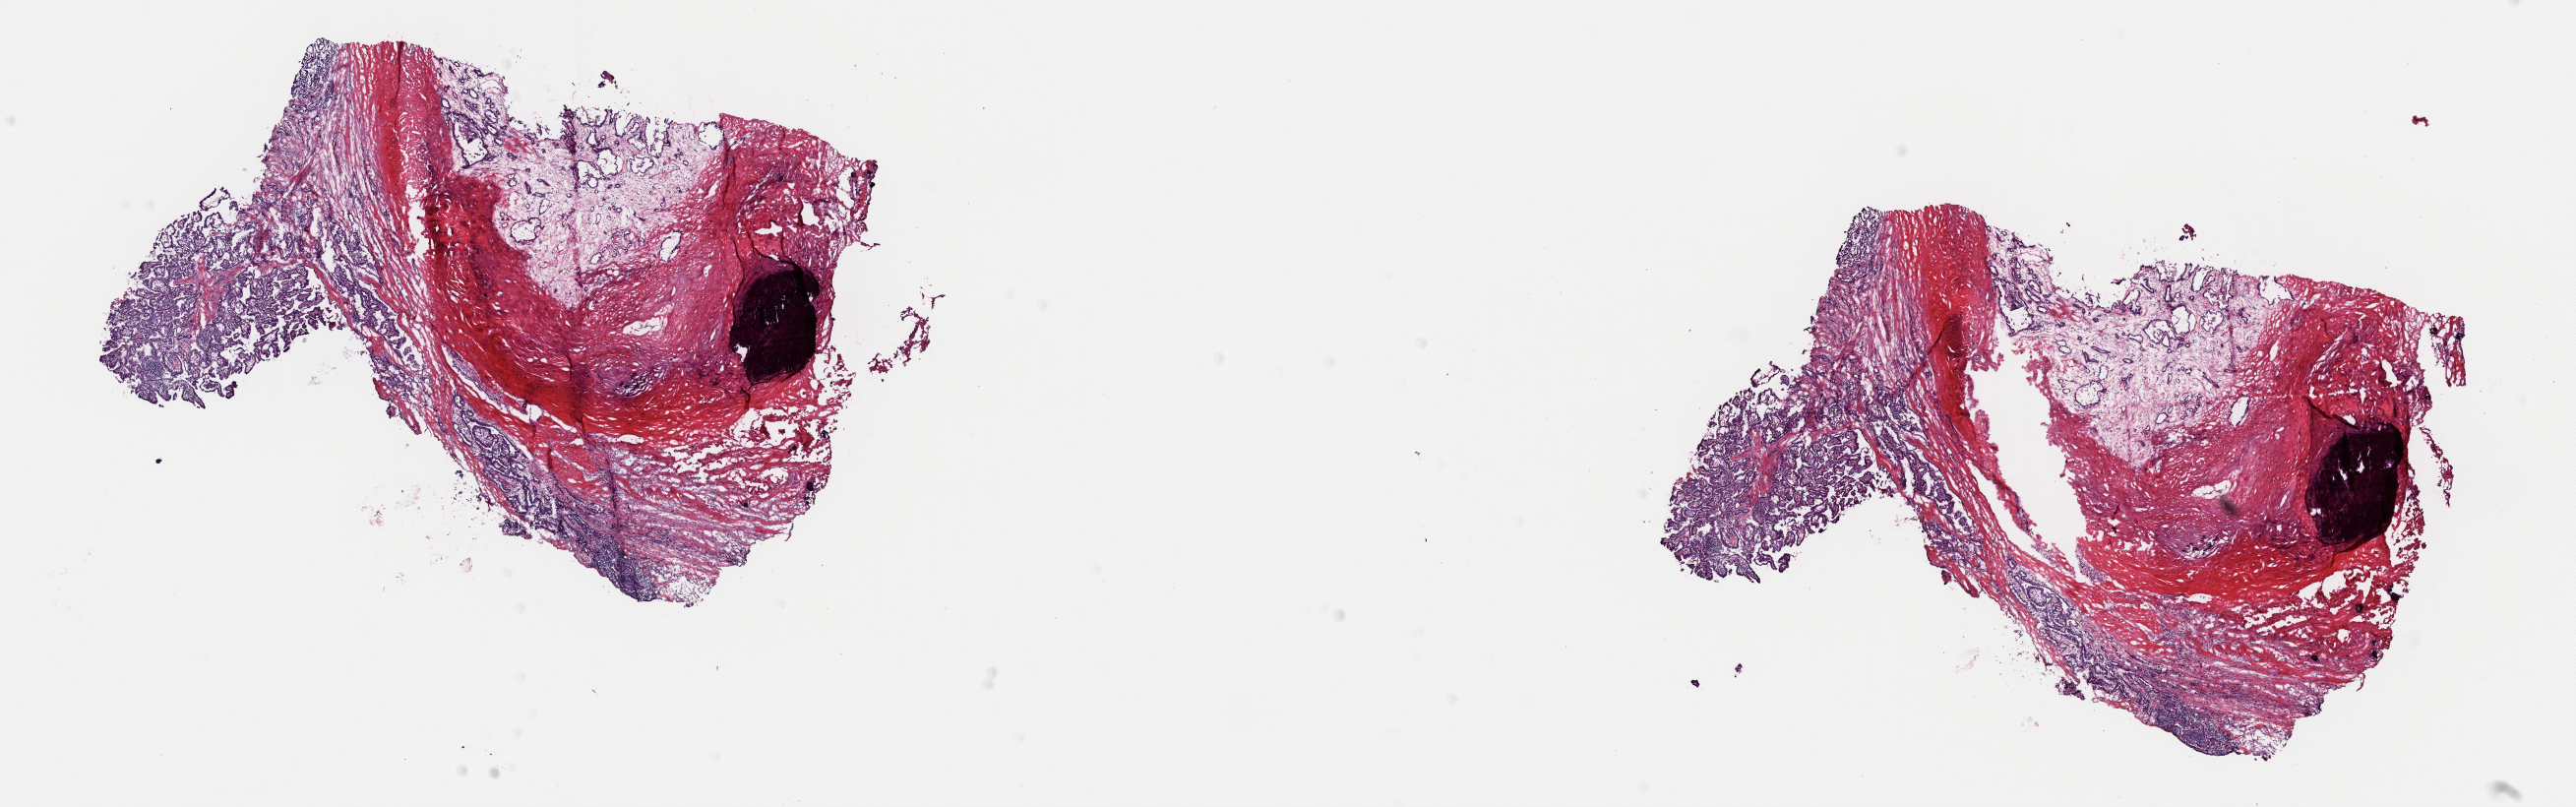
Digitized Hematoxylin and eosin (H&E) stained tissue section (whole slide) — a low-resolution overview of the entire scanned area, about 20.7 x 6.5 mm (acquisition: 40x scan). Frozen section from the top of the tissue portion. Primary tumour sample from the thyroid. Patient: male, age at initial diagnosis 83 years. Pathologist review of this section (percent, as recorded): tumour cells 40%, tumour nuclei 100%, normal cells 0%, stromal cells 60%, necrosis 0%. Inflammatory infiltration, as recorded: lymphocyte infiltration 6%, monocyte infiltration 1%, neutrophil infiltration 0%.
Diagnosis: Papillary adenocarcinoma, NOS (thyroid gland). Laterality: bilateral. AJCC pathologic stage: III. Lymph nodes positive (case pathology): 1 of 21 examined.